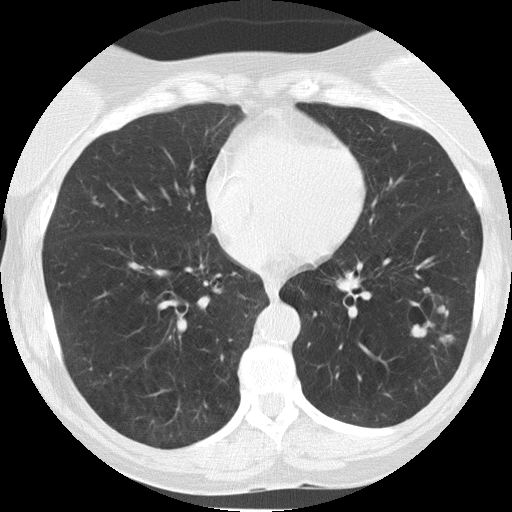
Low-dose screening chest CT, one axial slice. Position 64 of 149 along the scan axis. Reconstruction kernel FC51. 120 kVp. Lung window (W 1500 / L -600 HU). 2 mm slice thickness. 512 × 512 image matrix, field of view 290 × 290 mm.
Structures marked on this image (expert manual segmentation):
- lesion 1 (tumor, lower lobe of left lung): bounding box (x1, y1, x2, y2) in pixels: (411, 305, 454, 345)